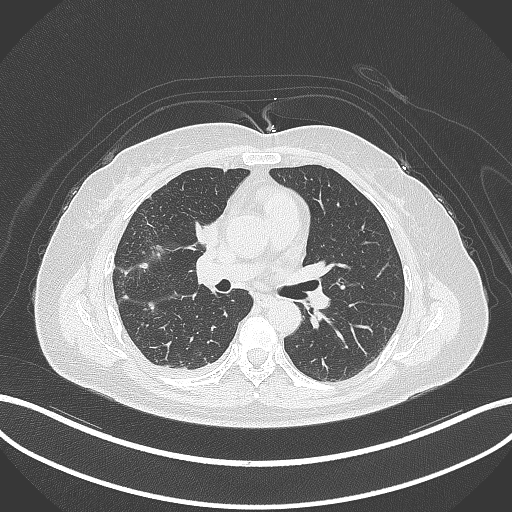
Chest CT, one axial slice. Slice 152 of 305 in the series (ordered by position). Reconstruction kernel B70f. 120 kVp. Lung window (W 1500 / L -600 HU). 1 mm slice thickness. 512 × 512 image matrix, field of view 400 × 400 mm. Female patient, age 52 years. From the clinical record (not read from this slice): clinical TNM (as recorded): T3 N1 M1.
Annotated regions visible in this slice (bounding box drawn by a radiologist):
- lung tumour (recorded histology: adenocarcinoma): bounding box <189,217,223,257> (left, top, right, bottom; pixels)